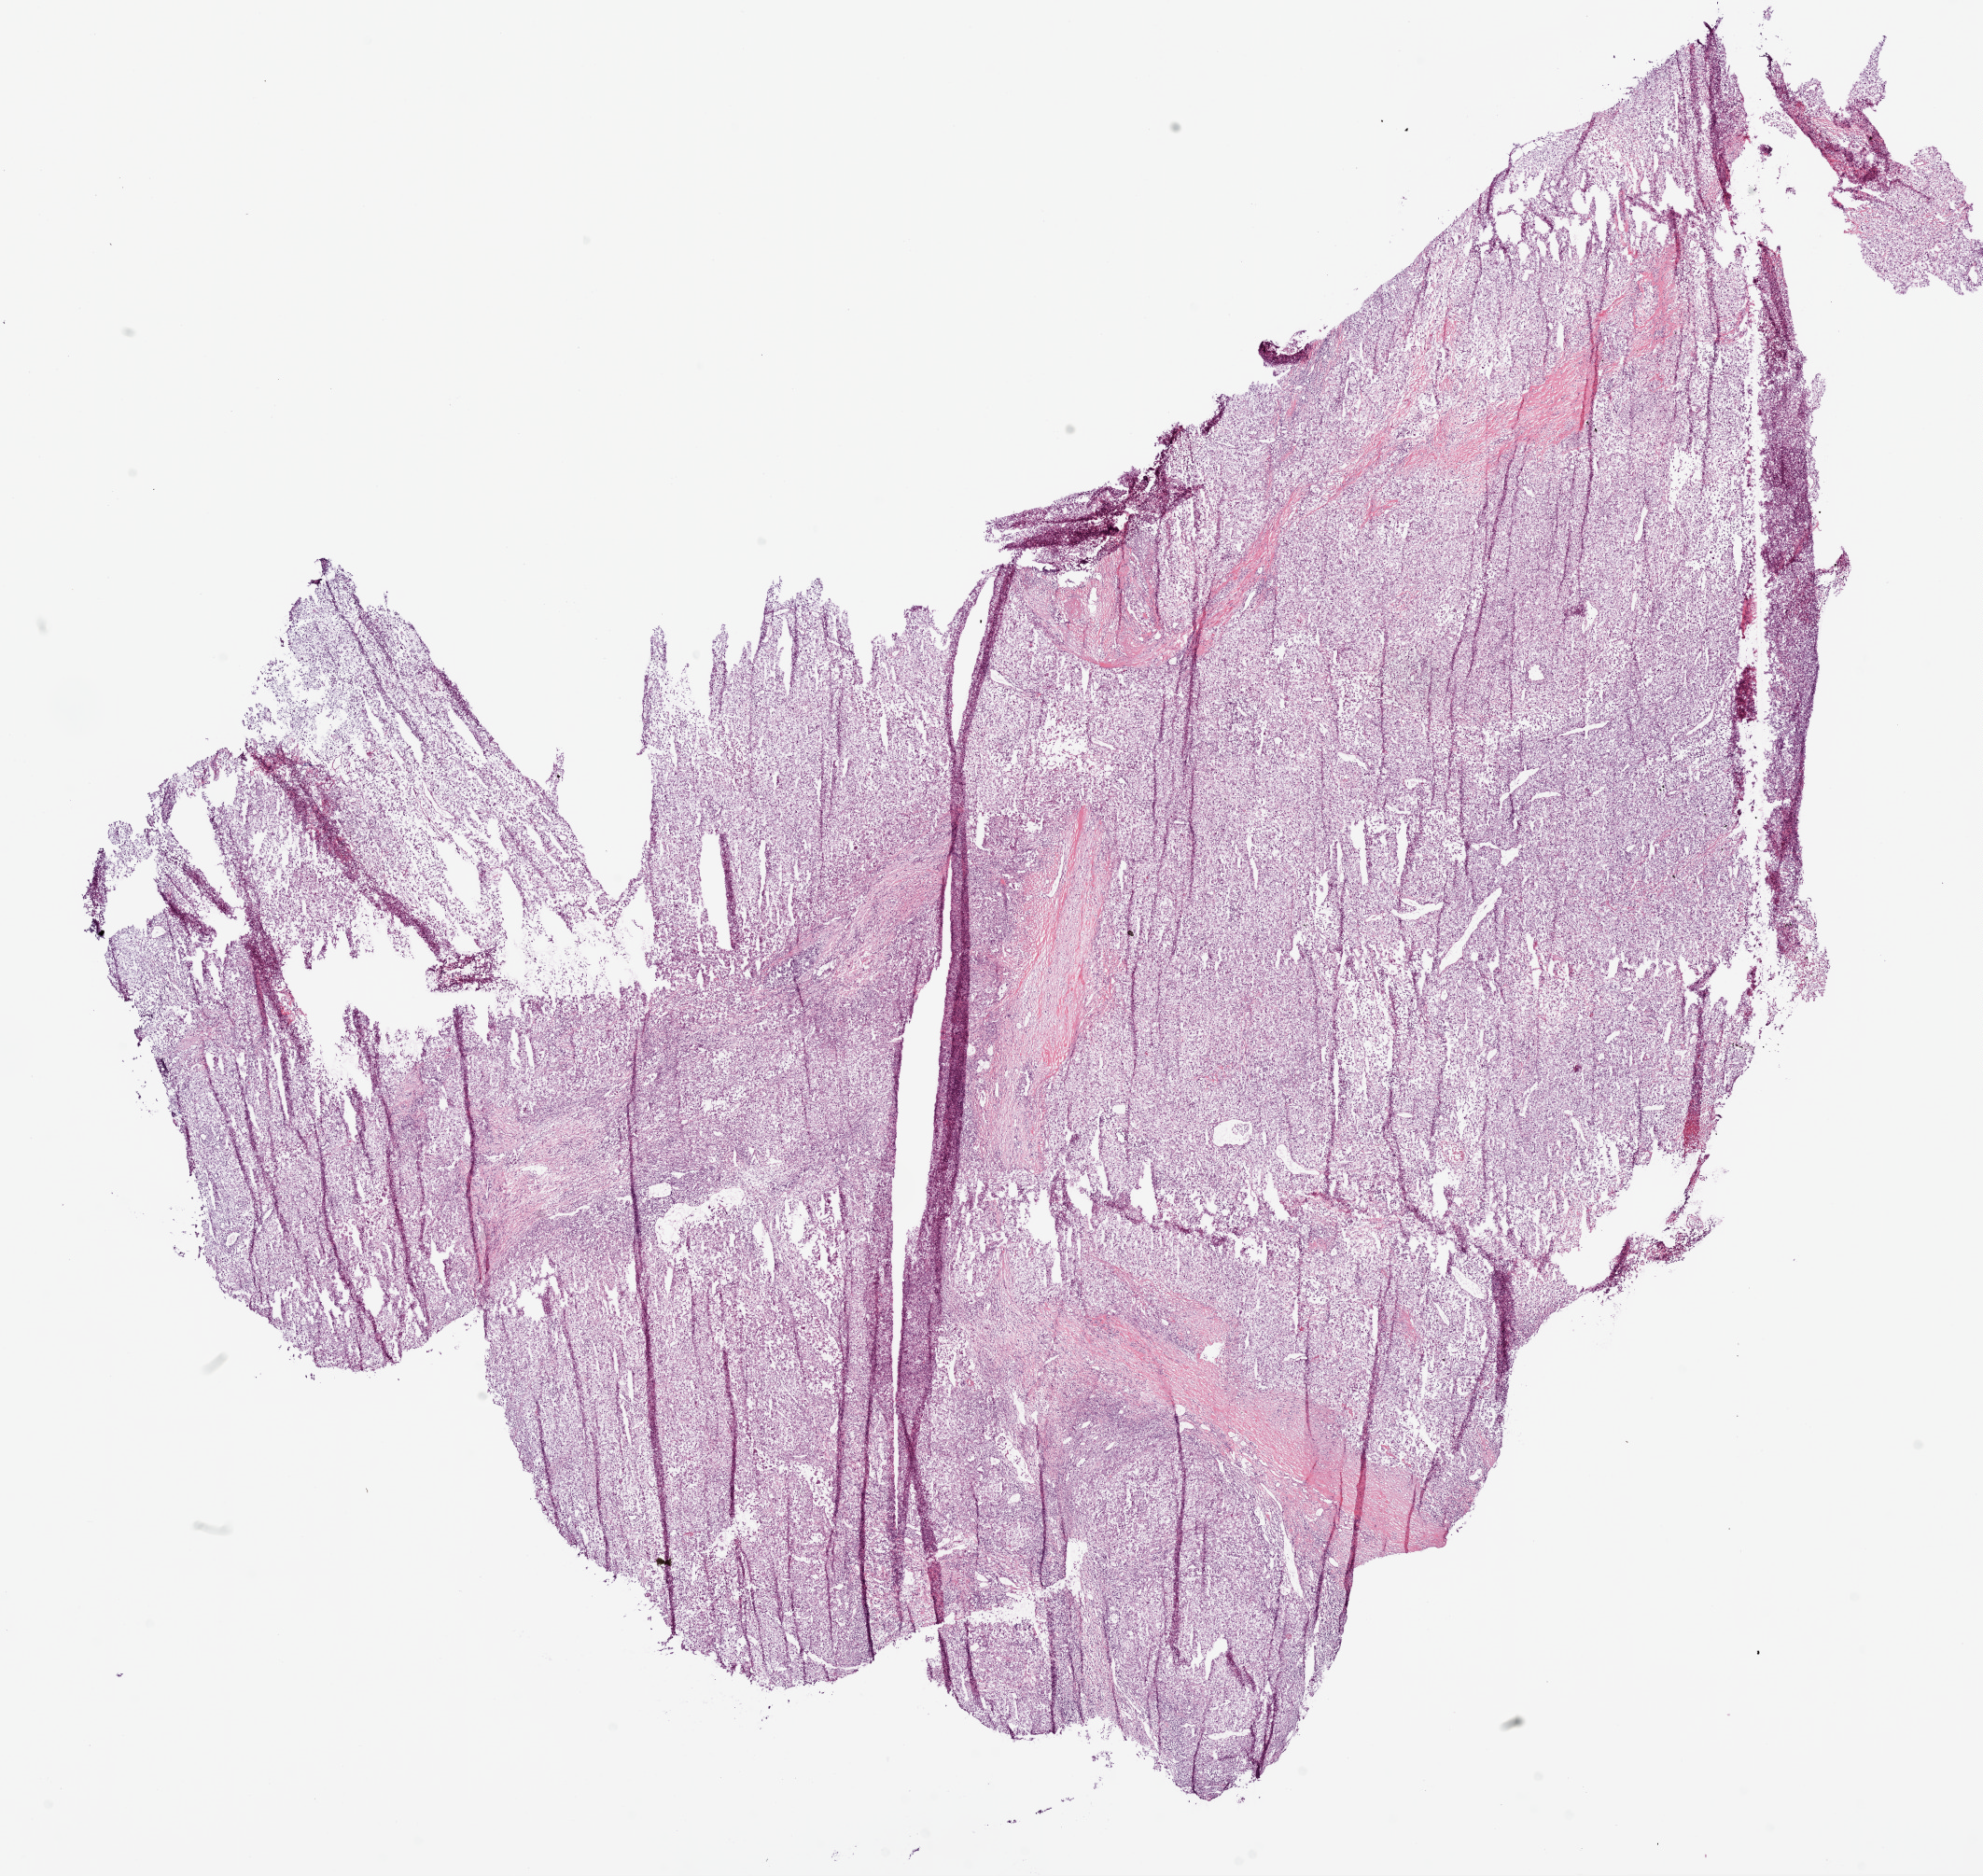
Whole-slide histology image, H&E — low-resolution overview of the scanned area, about 17.1 x 16.1 mm; frozen section; kidney, primary tumour sample. Female, age 67 years at initial diagnosis. Histologic grade: G4 (undifferentiated). Pathologist review of this section (percent, as recorded): tumour cells 85%, tumour nuclei 85%, normal cells 0%, stromal cells 15%, necrosis 0%.
AJCC pathologic stage: III. Laterality: right. Diagnosis: Clear cell adenocarcinoma, NOS.